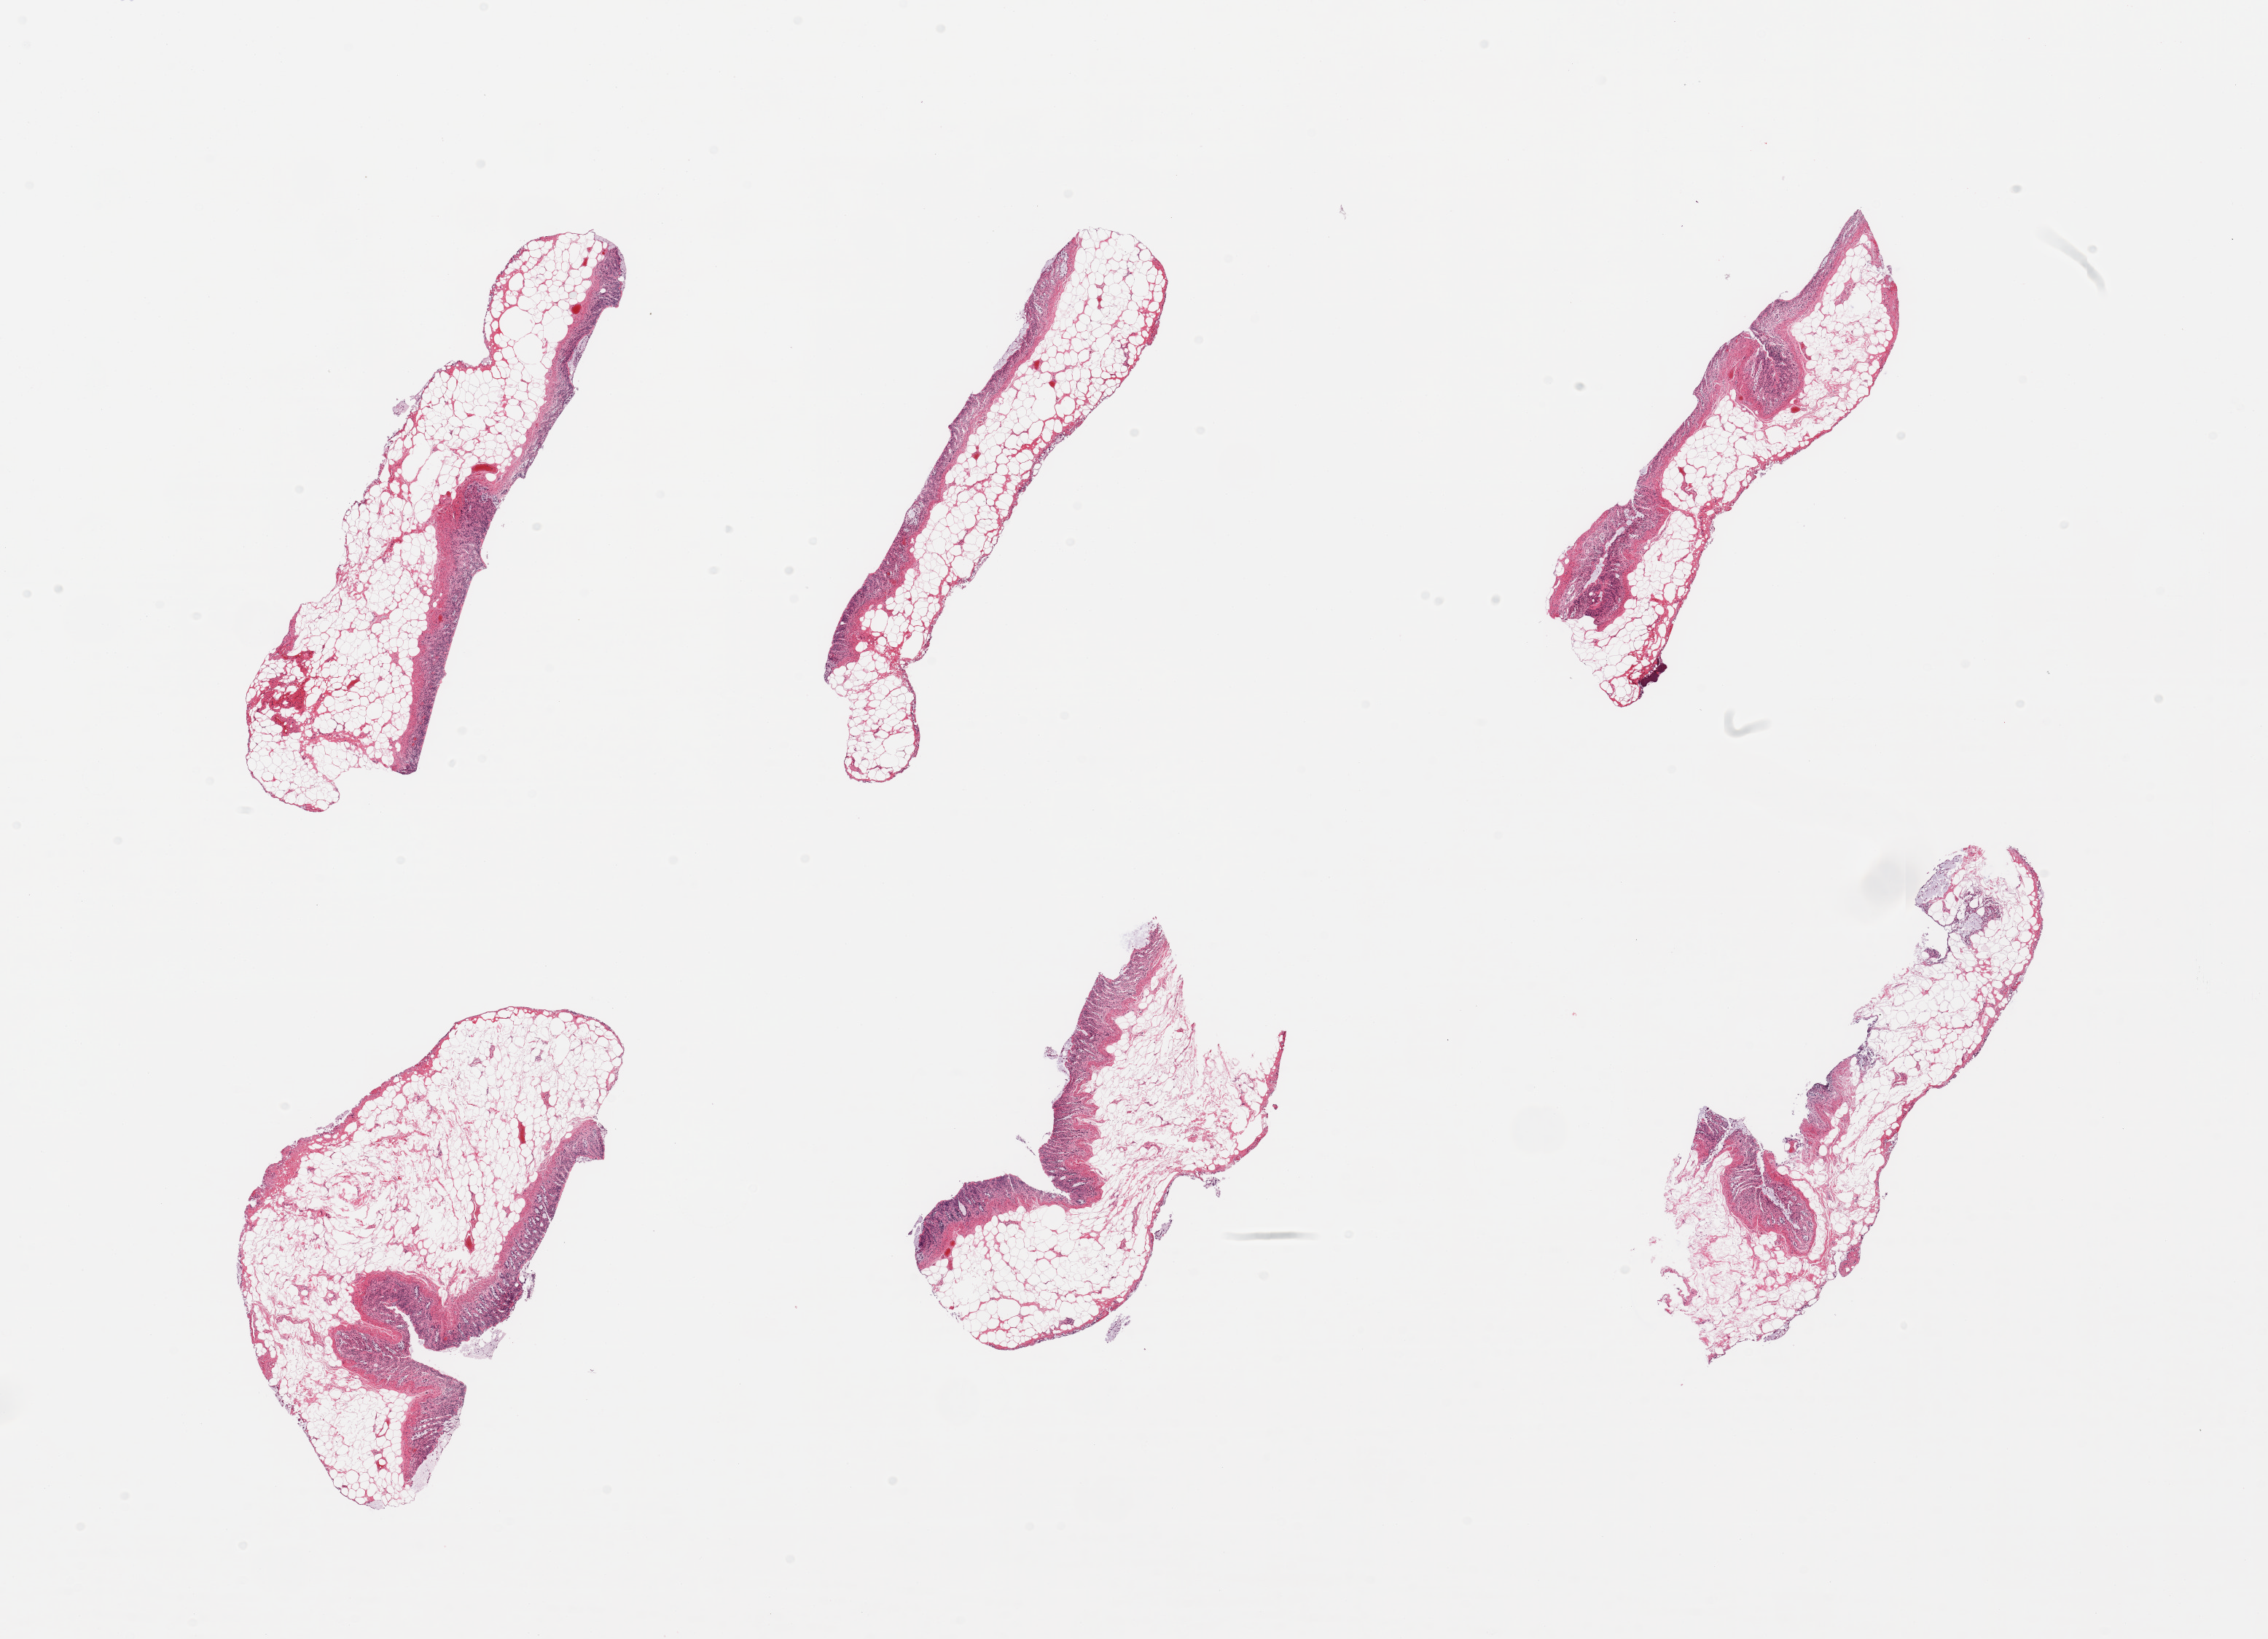
Whole-slide image, hematoxylin and eosin (H&E) stain, brightfield — low-resolution overview of the scanned area, about 24.6 x 17.8 mm (slide scanned at 20x); PAXgene-fixed, paraffin-embedded tissue; sampled site (target tissue): sigmoid colon; tissue donor sample. Donor: male.
Review note (as recorded): 6 pieces; severely autolyzed mucosa and lack of muscularis.